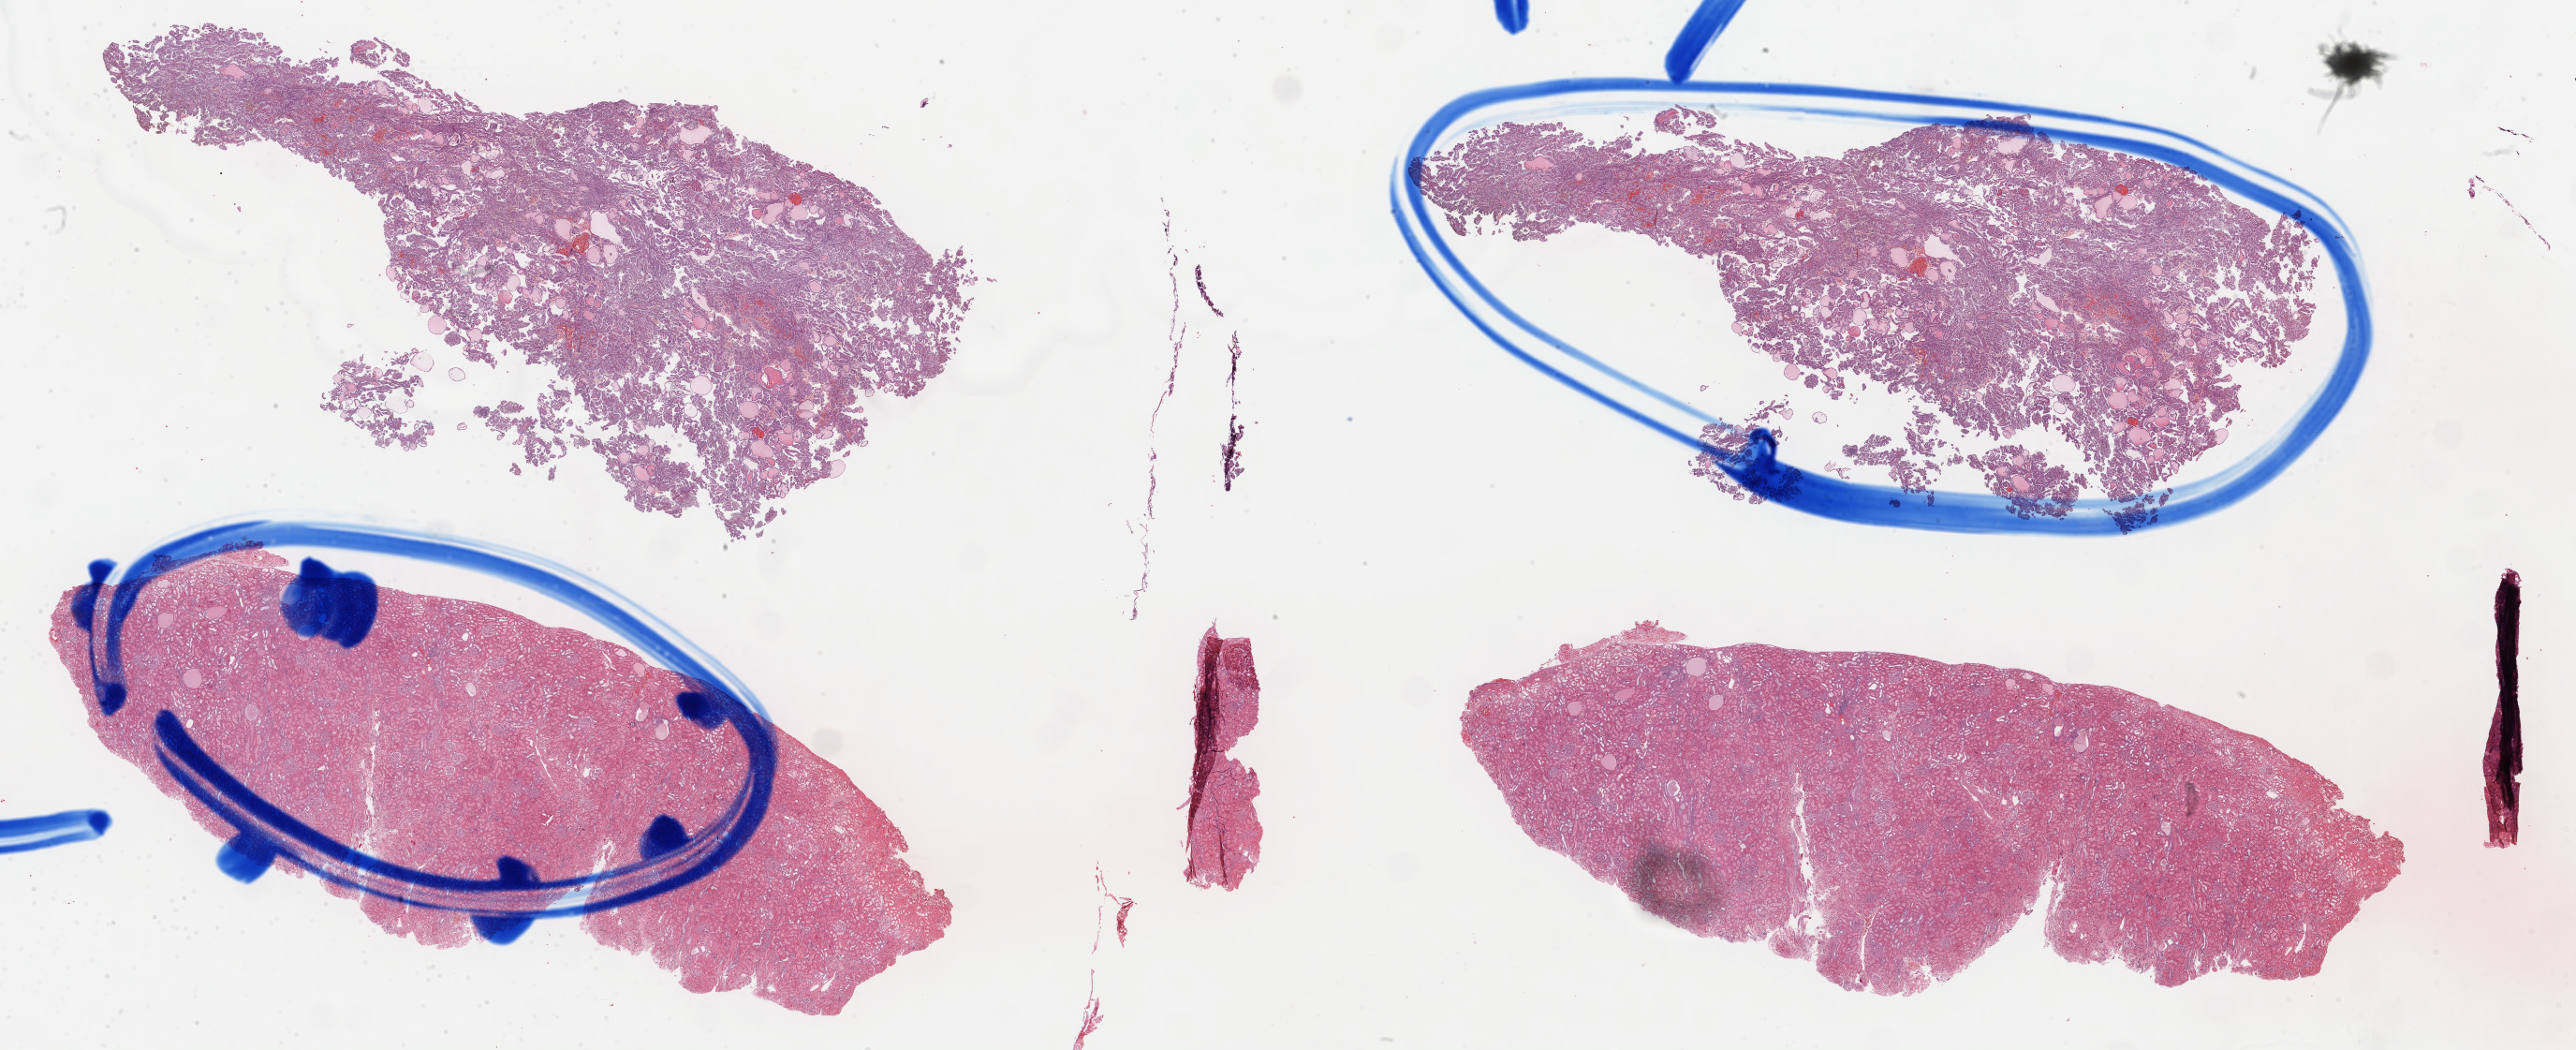
Digitized H&E tissue section (whole slide) — whole scanned area (about 43.4 x 17.7 mm) shown as a low-resolution overview, formalin-fixed paraffin-embedded (FFPE) diagnostic section, kidney, primary tumour sample. Patient: male, age at initial diagnosis 57 years.
Histologic diagnosis: Papillary adenocarcinoma, NOS.